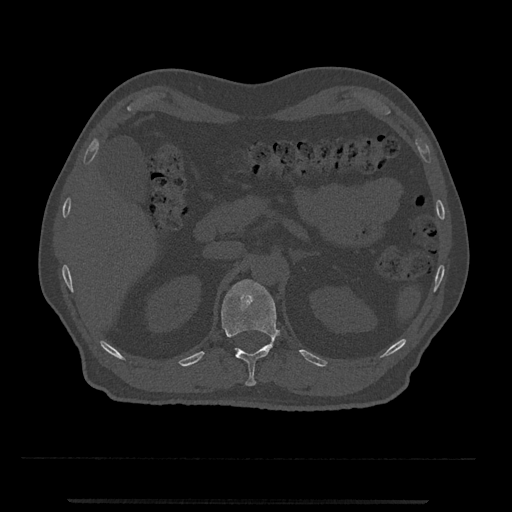
CT including the spine, one axial slice; slice 392 of 797 in the series (ordered by position); reconstruction kernel Br40s/3; bone window (W 1800 / L 400 HU); 512 × 512 image matrix. Patient: male, 63 years. From the clinical record (not read from this slice): primary cancer: prostate.
Annotated regions visible in this slice (semi-automatic segmentation, software-assisted and operator-edited):
- T12 vertebra: box from (x=221, y=279) to (x=280, y=386) px